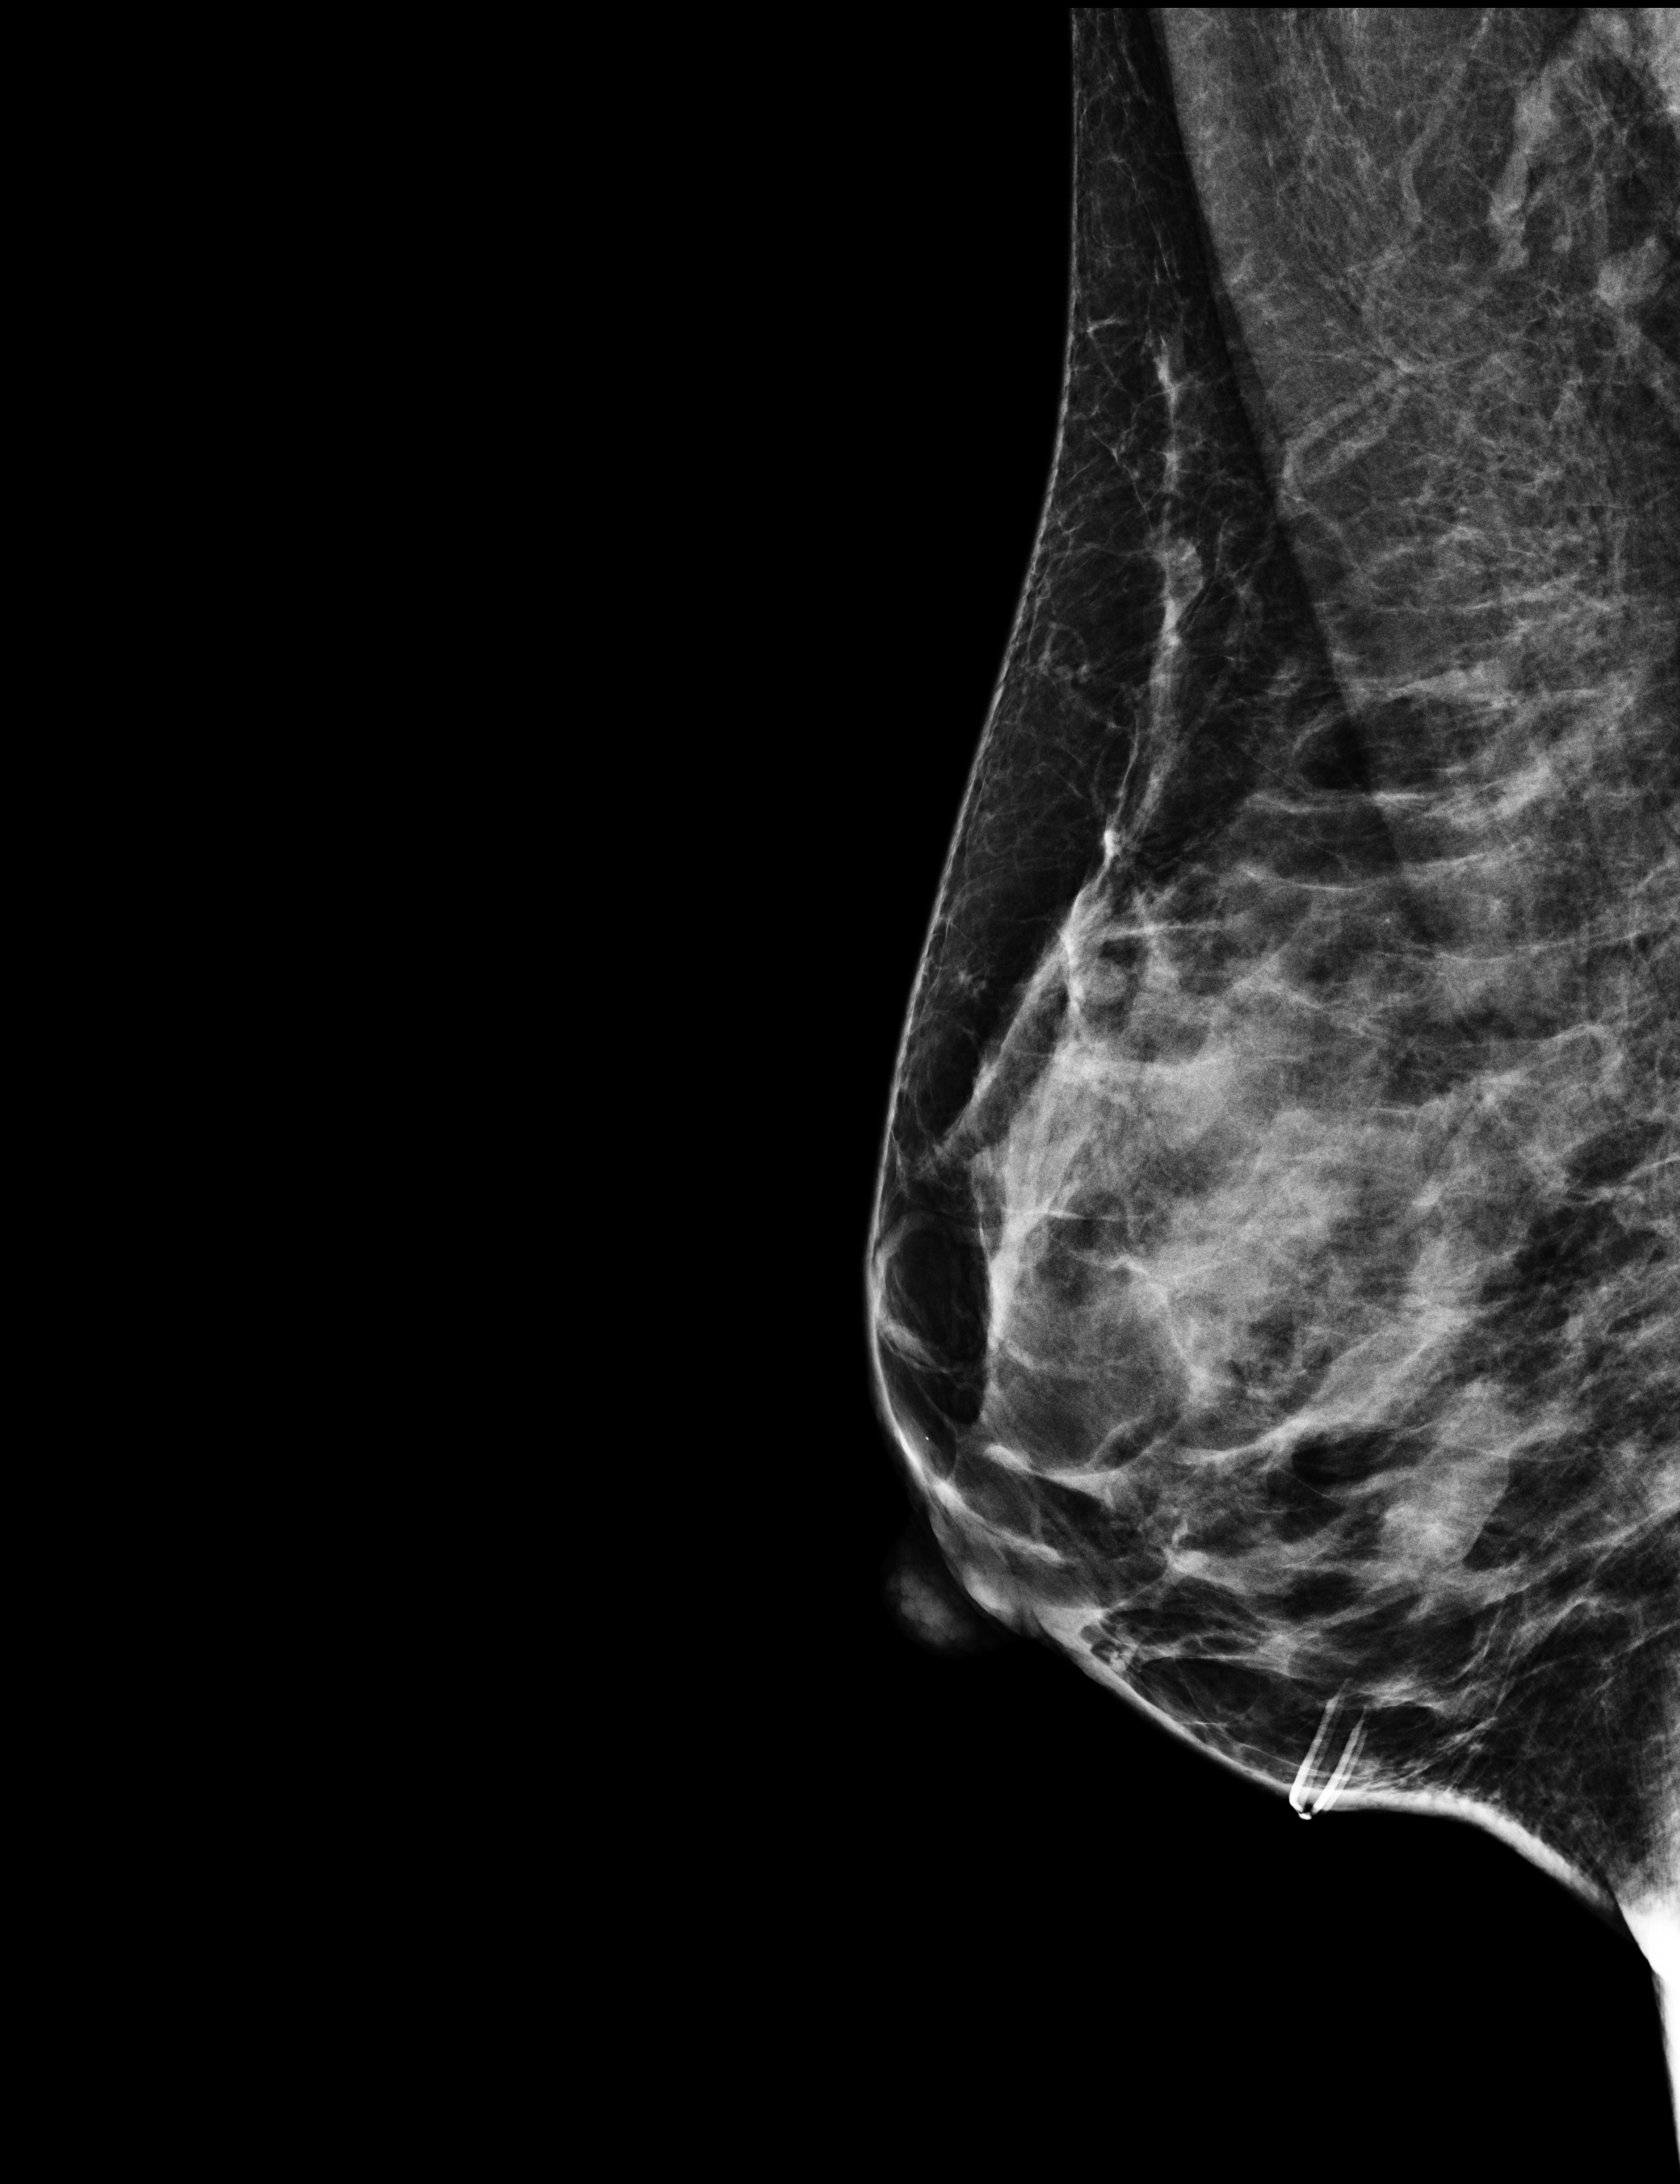
Digital mammogram (FFDM), right breast, medio-lateral oblique projection, annual screening mammography examination, compressed breast thickness 45 mm. Patient aged 49 years (female).
Breast density at the screening exam (both breasts): heterogeneously dense (BI-RADS density category c). Final BI-RADS category for the screening round (tomosynthesis exam, both breasts): category 1. Recall: no recall after this screen.